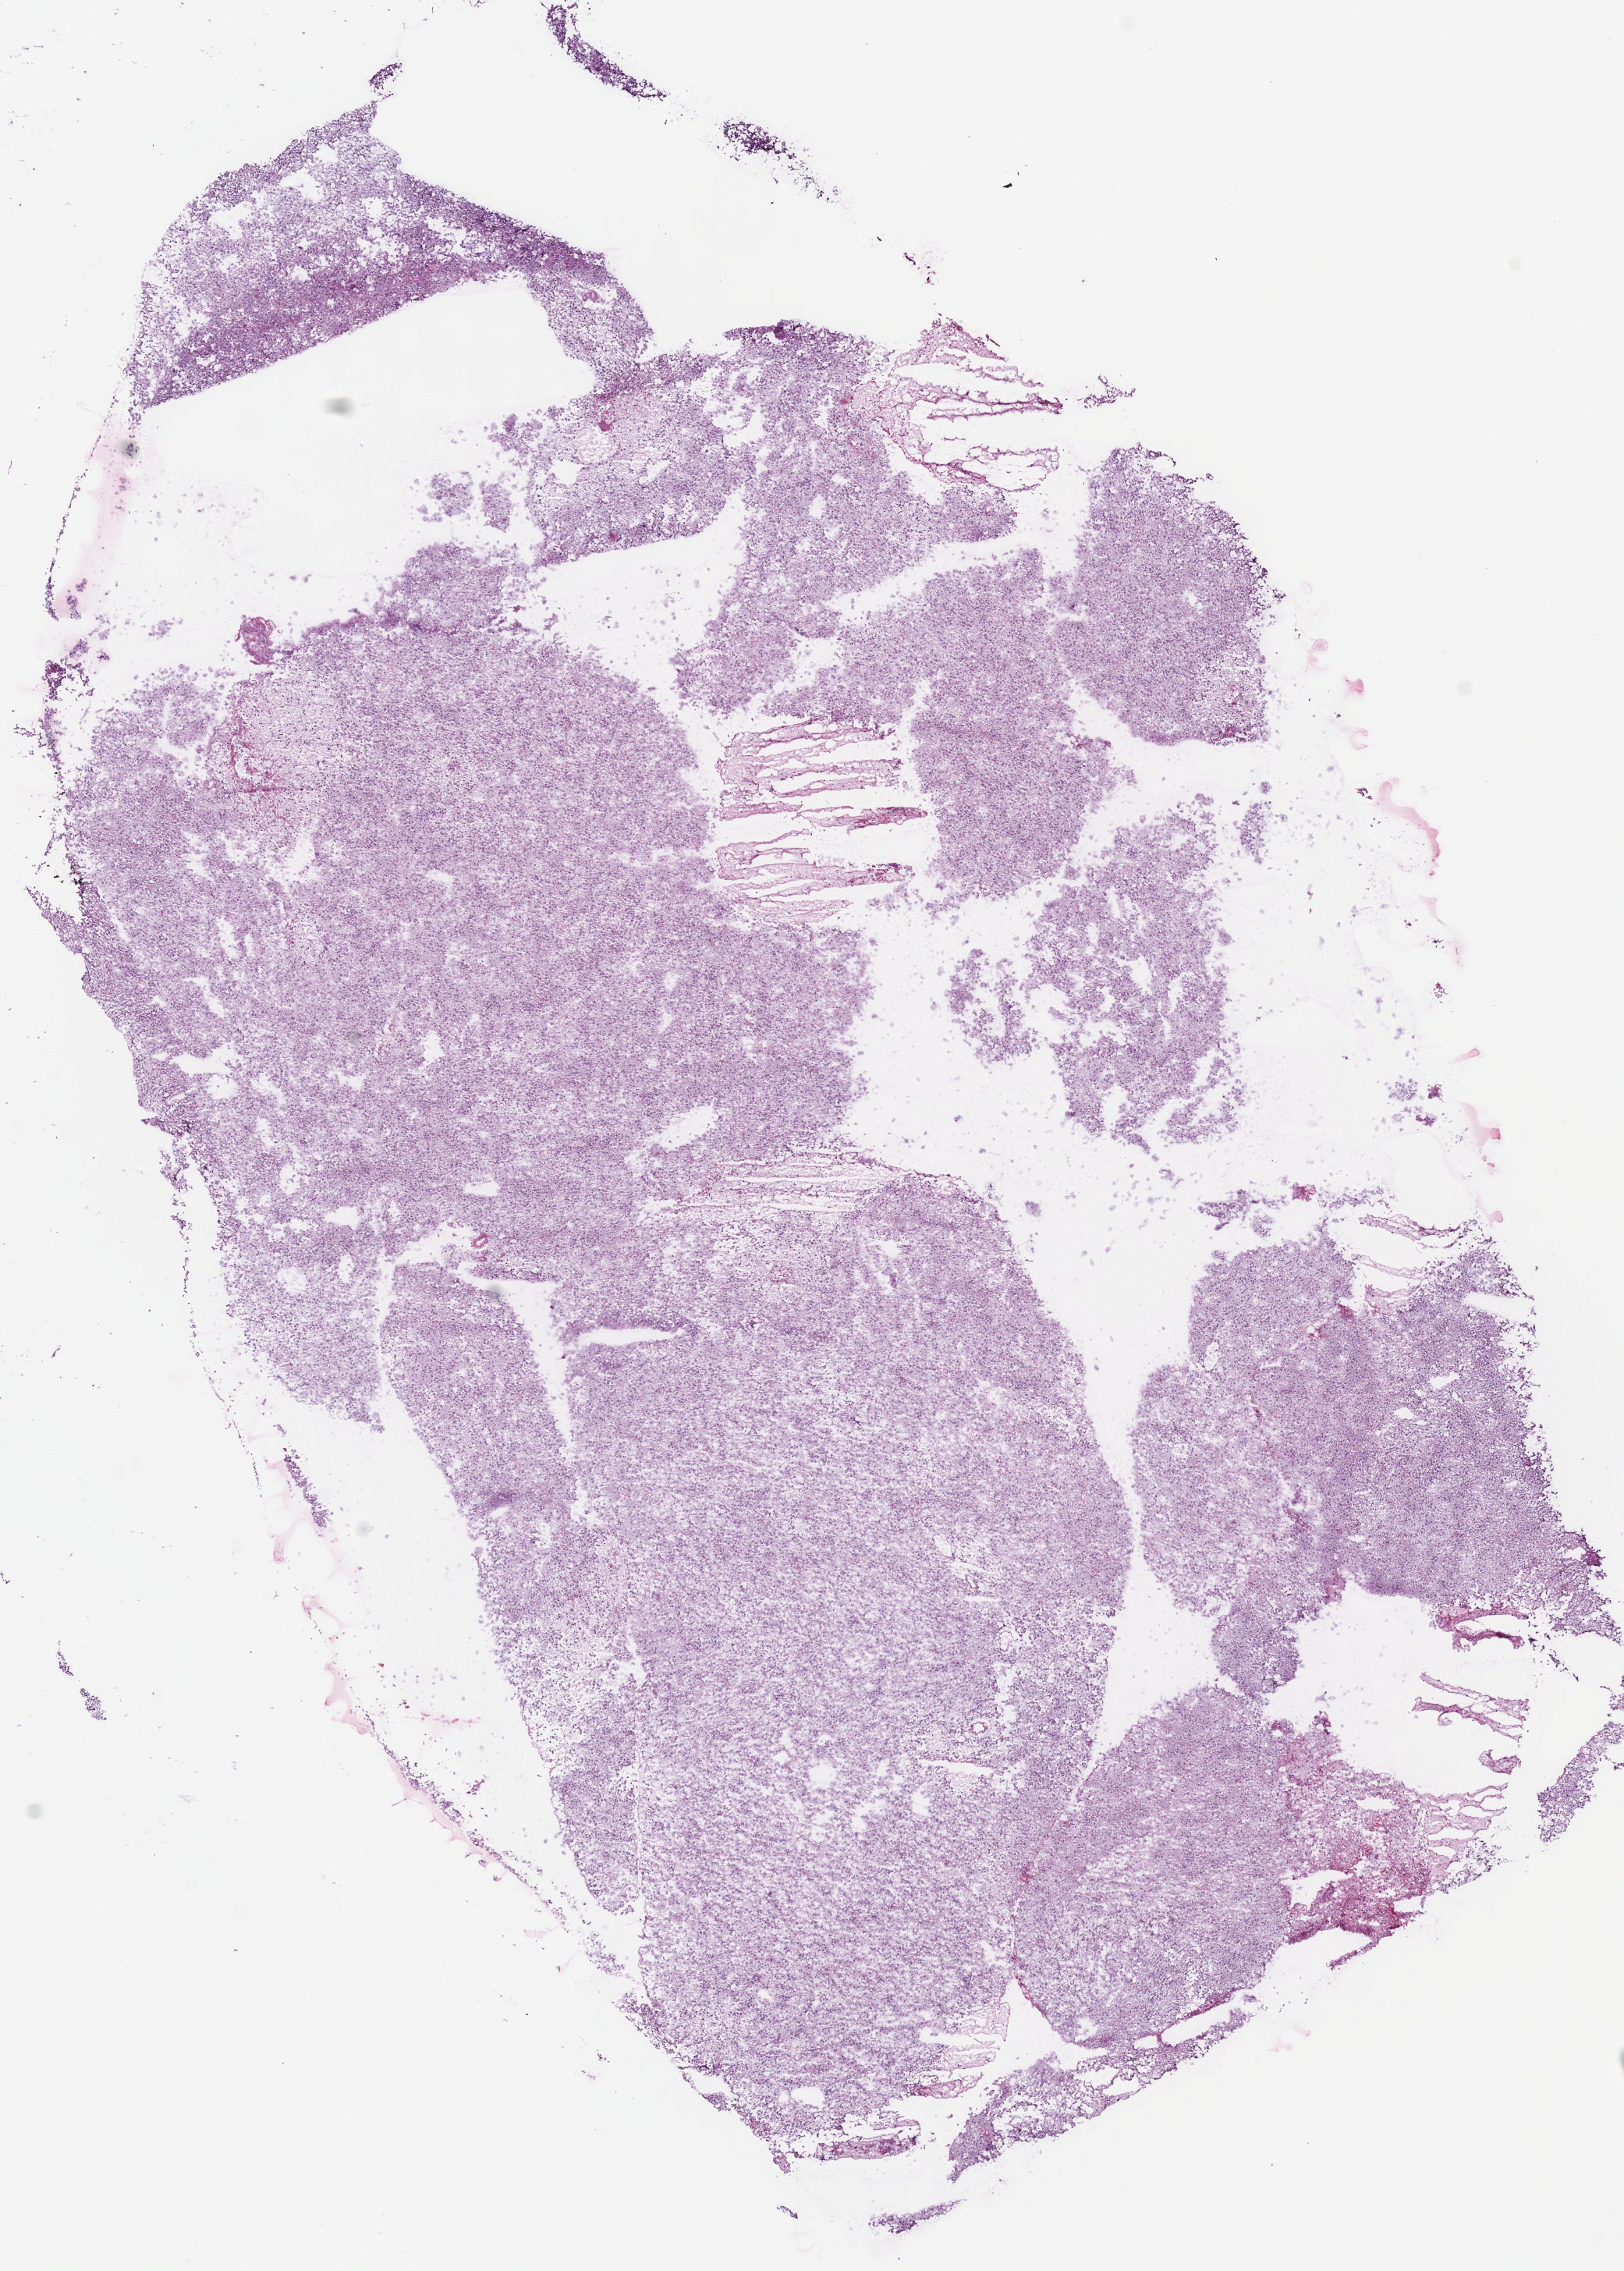
H&E-stained whole-slide image — whole scanned area (about 8.2 x 11.5 mm, from a 40x scan) shown as a low-resolution overview. Frozen section from the bottom of the tissue portion. Brain, primary tumour sample. Male, age 35 years at initial diagnosis. Histologic grade: G2 (moderately differentiated). Slide review estimates, as recorded: tumour cells 100%, tumour nuclei 80%, normal cells 0%, stromal cells 0%, necrosis 0%.
Diagnosis: Oligodendroglioma, NOS (cerebrum). Laterality: right.